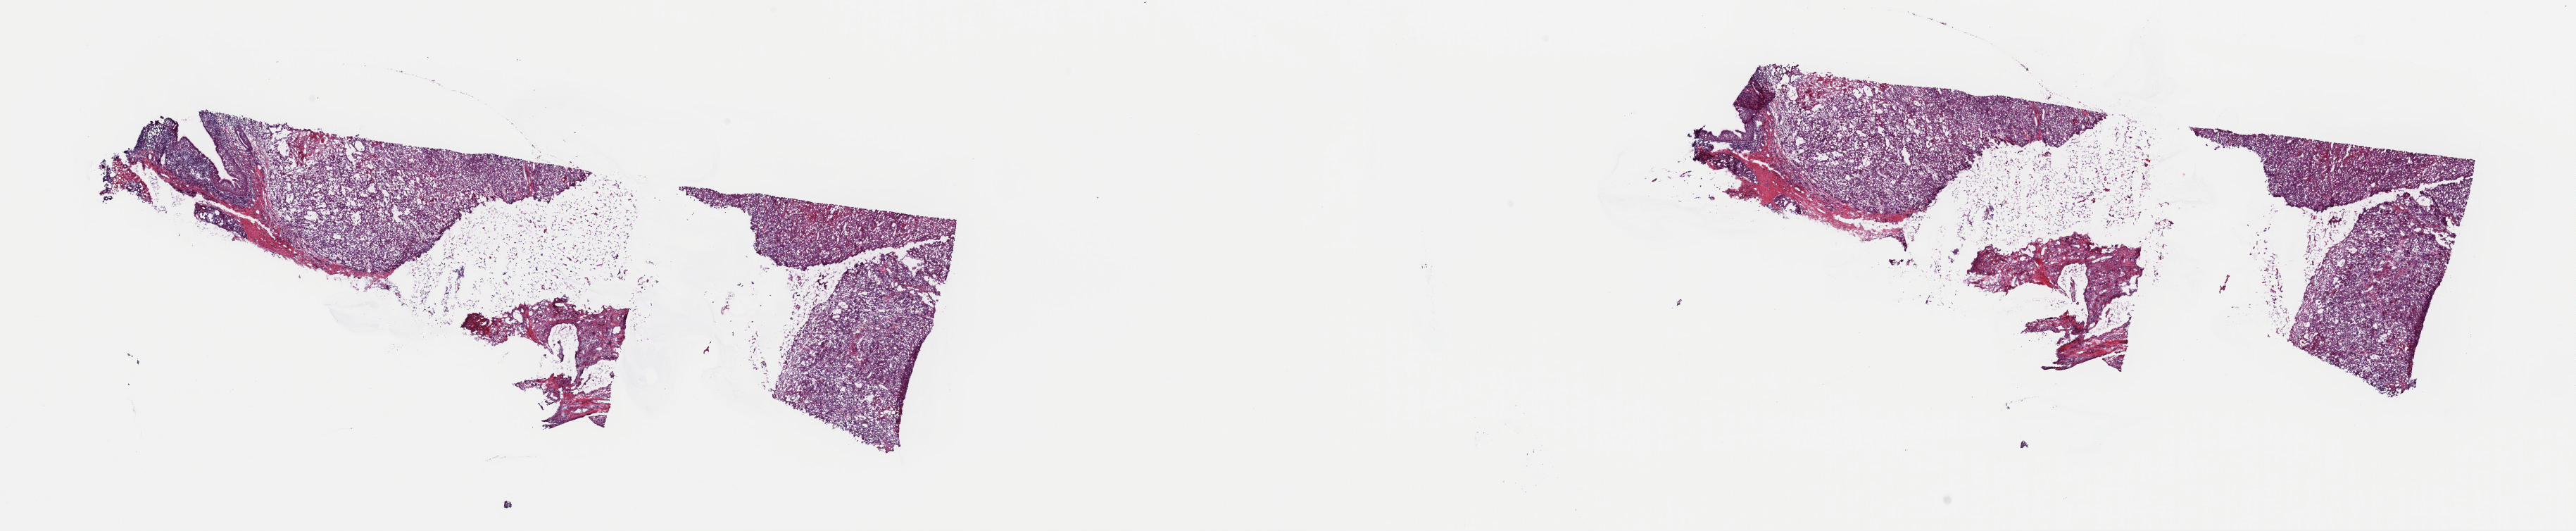
Digitized H&E-stained tissue section (whole slide), low-resolution overview of the scanned area, about 28.9 x 6.0 mm. Frozen section. Sample: primary tumour, head and neck. Male, age 75 years at initial diagnosis. Histologic grade: G1 (well differentiated). Pathologist review of this section (percent, as recorded): tumour cells 100%, tumour nuclei 75%, normal cells 0%, stromal cells 0%, necrosis 0%. Infiltration values recorded for this section: lymphocyte infiltration 8%, monocyte infiltration 0%, neutrophil infiltration 1%.
Histologic diagnosis: Squamous cell carcinoma, keratinizing, NOS. AJCC pathologic stage: III (7th edition).